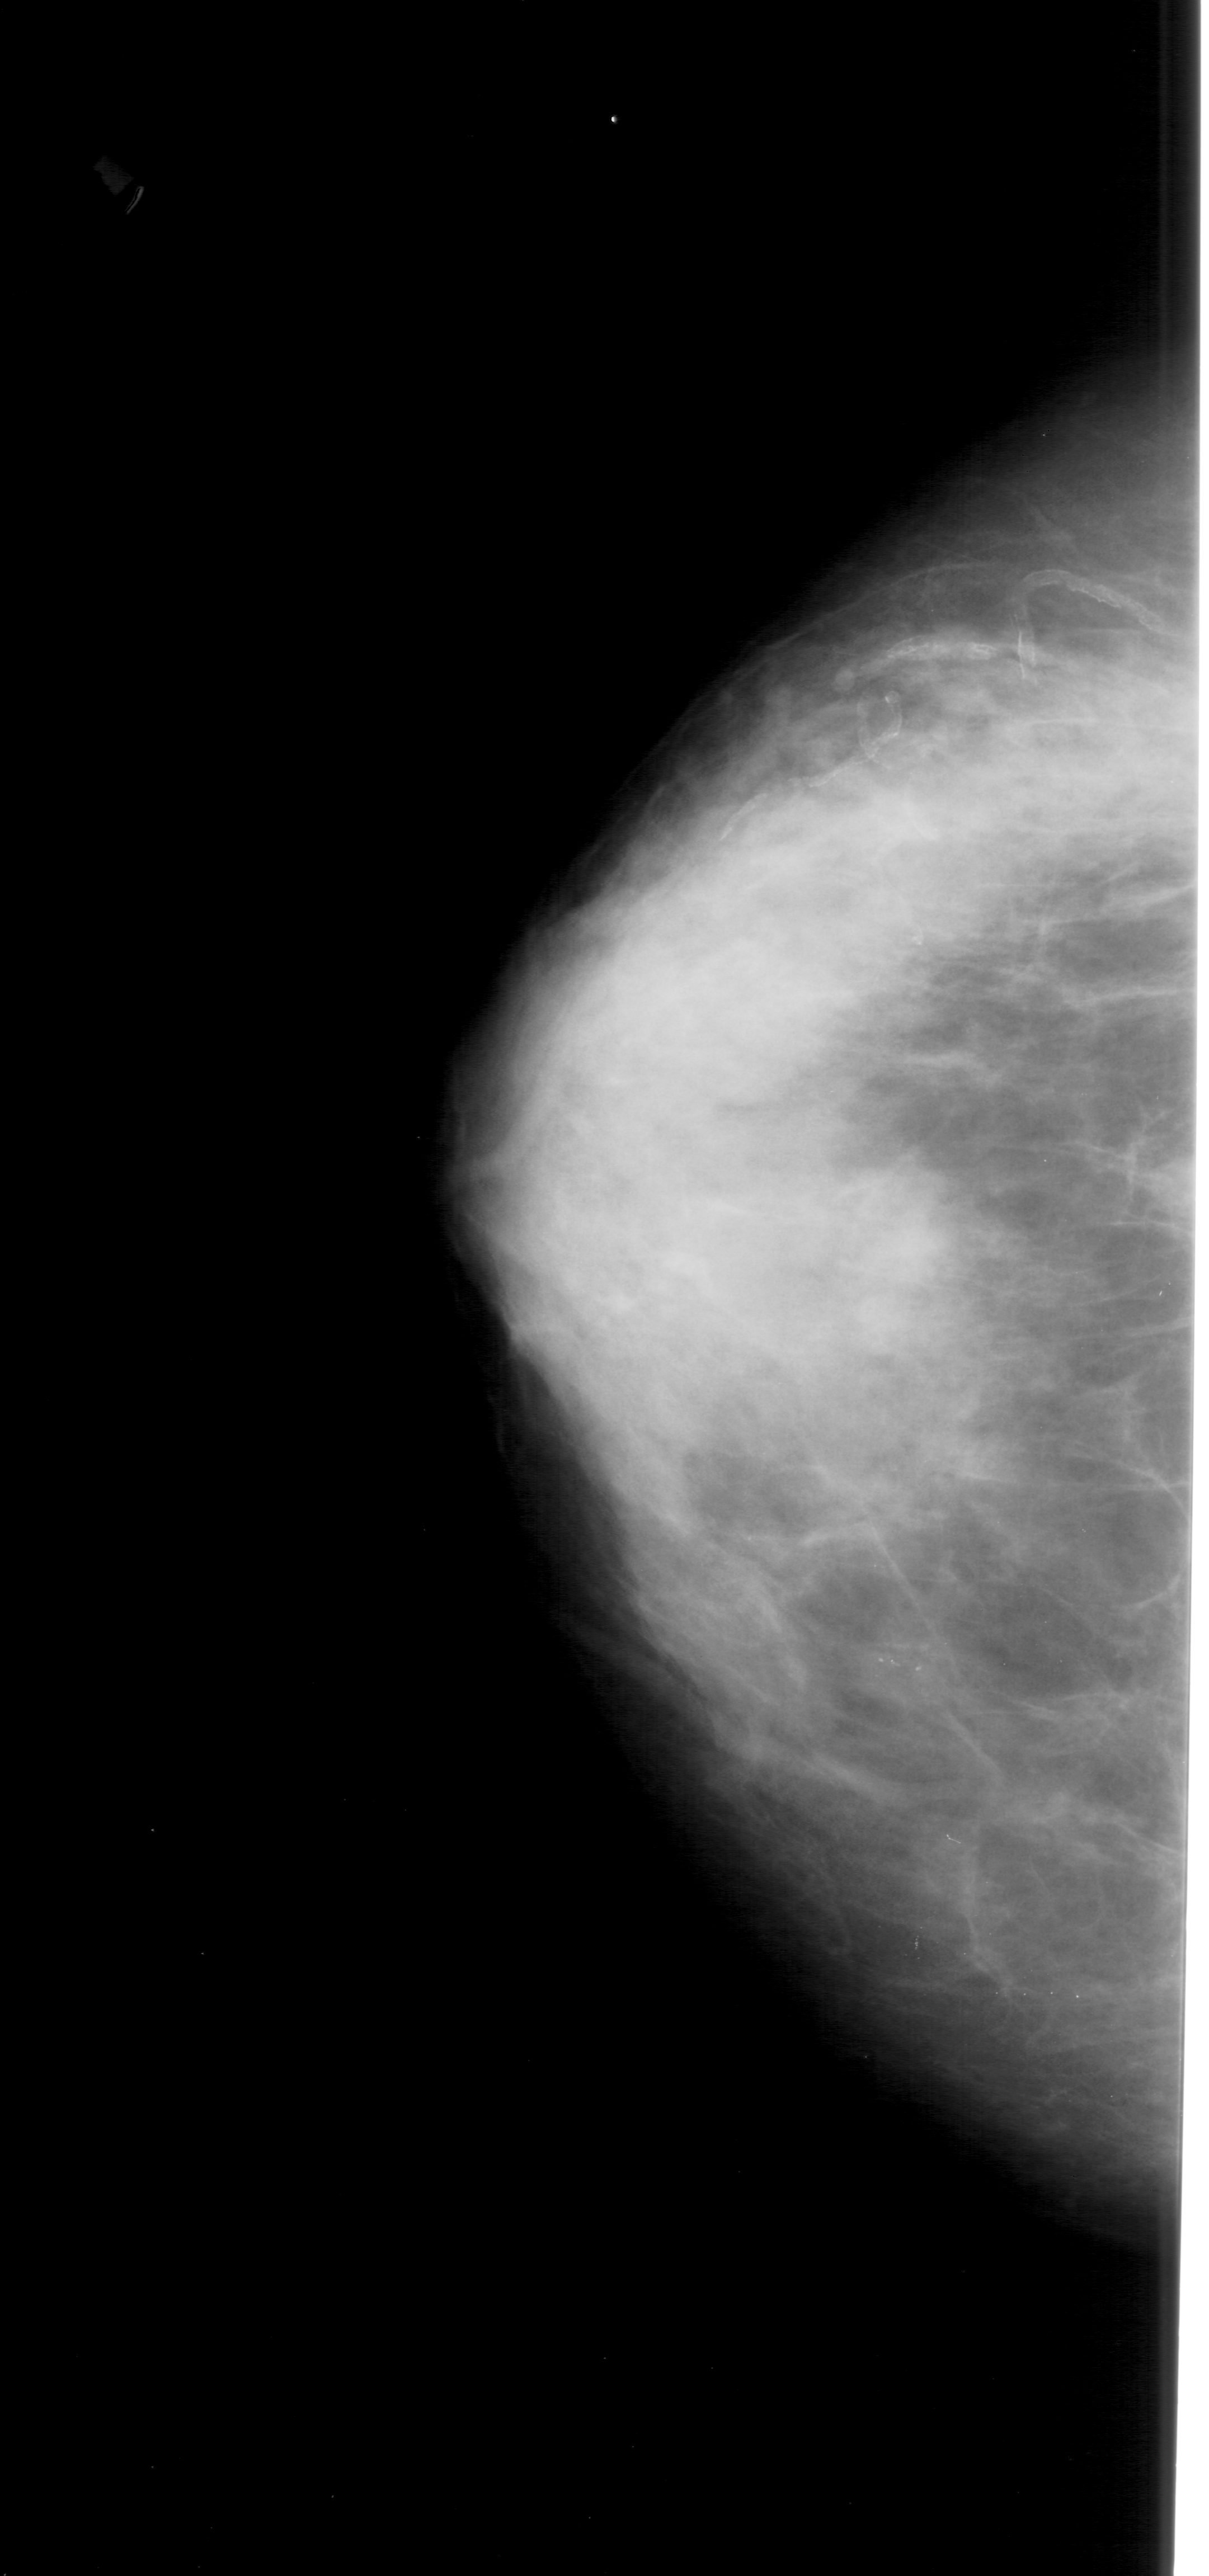
Digitized screen-film mammogram, left breast, craniocaudal (CC) view, BI-RADS breast density category 4 (scale 1–4).
Radiologist-marked abnormalities on this image: calcifications, morphology pleomorphic, distribution clustered; BI-RADS assessment category 4; pathology result (as recorded, not read from the image): benign.